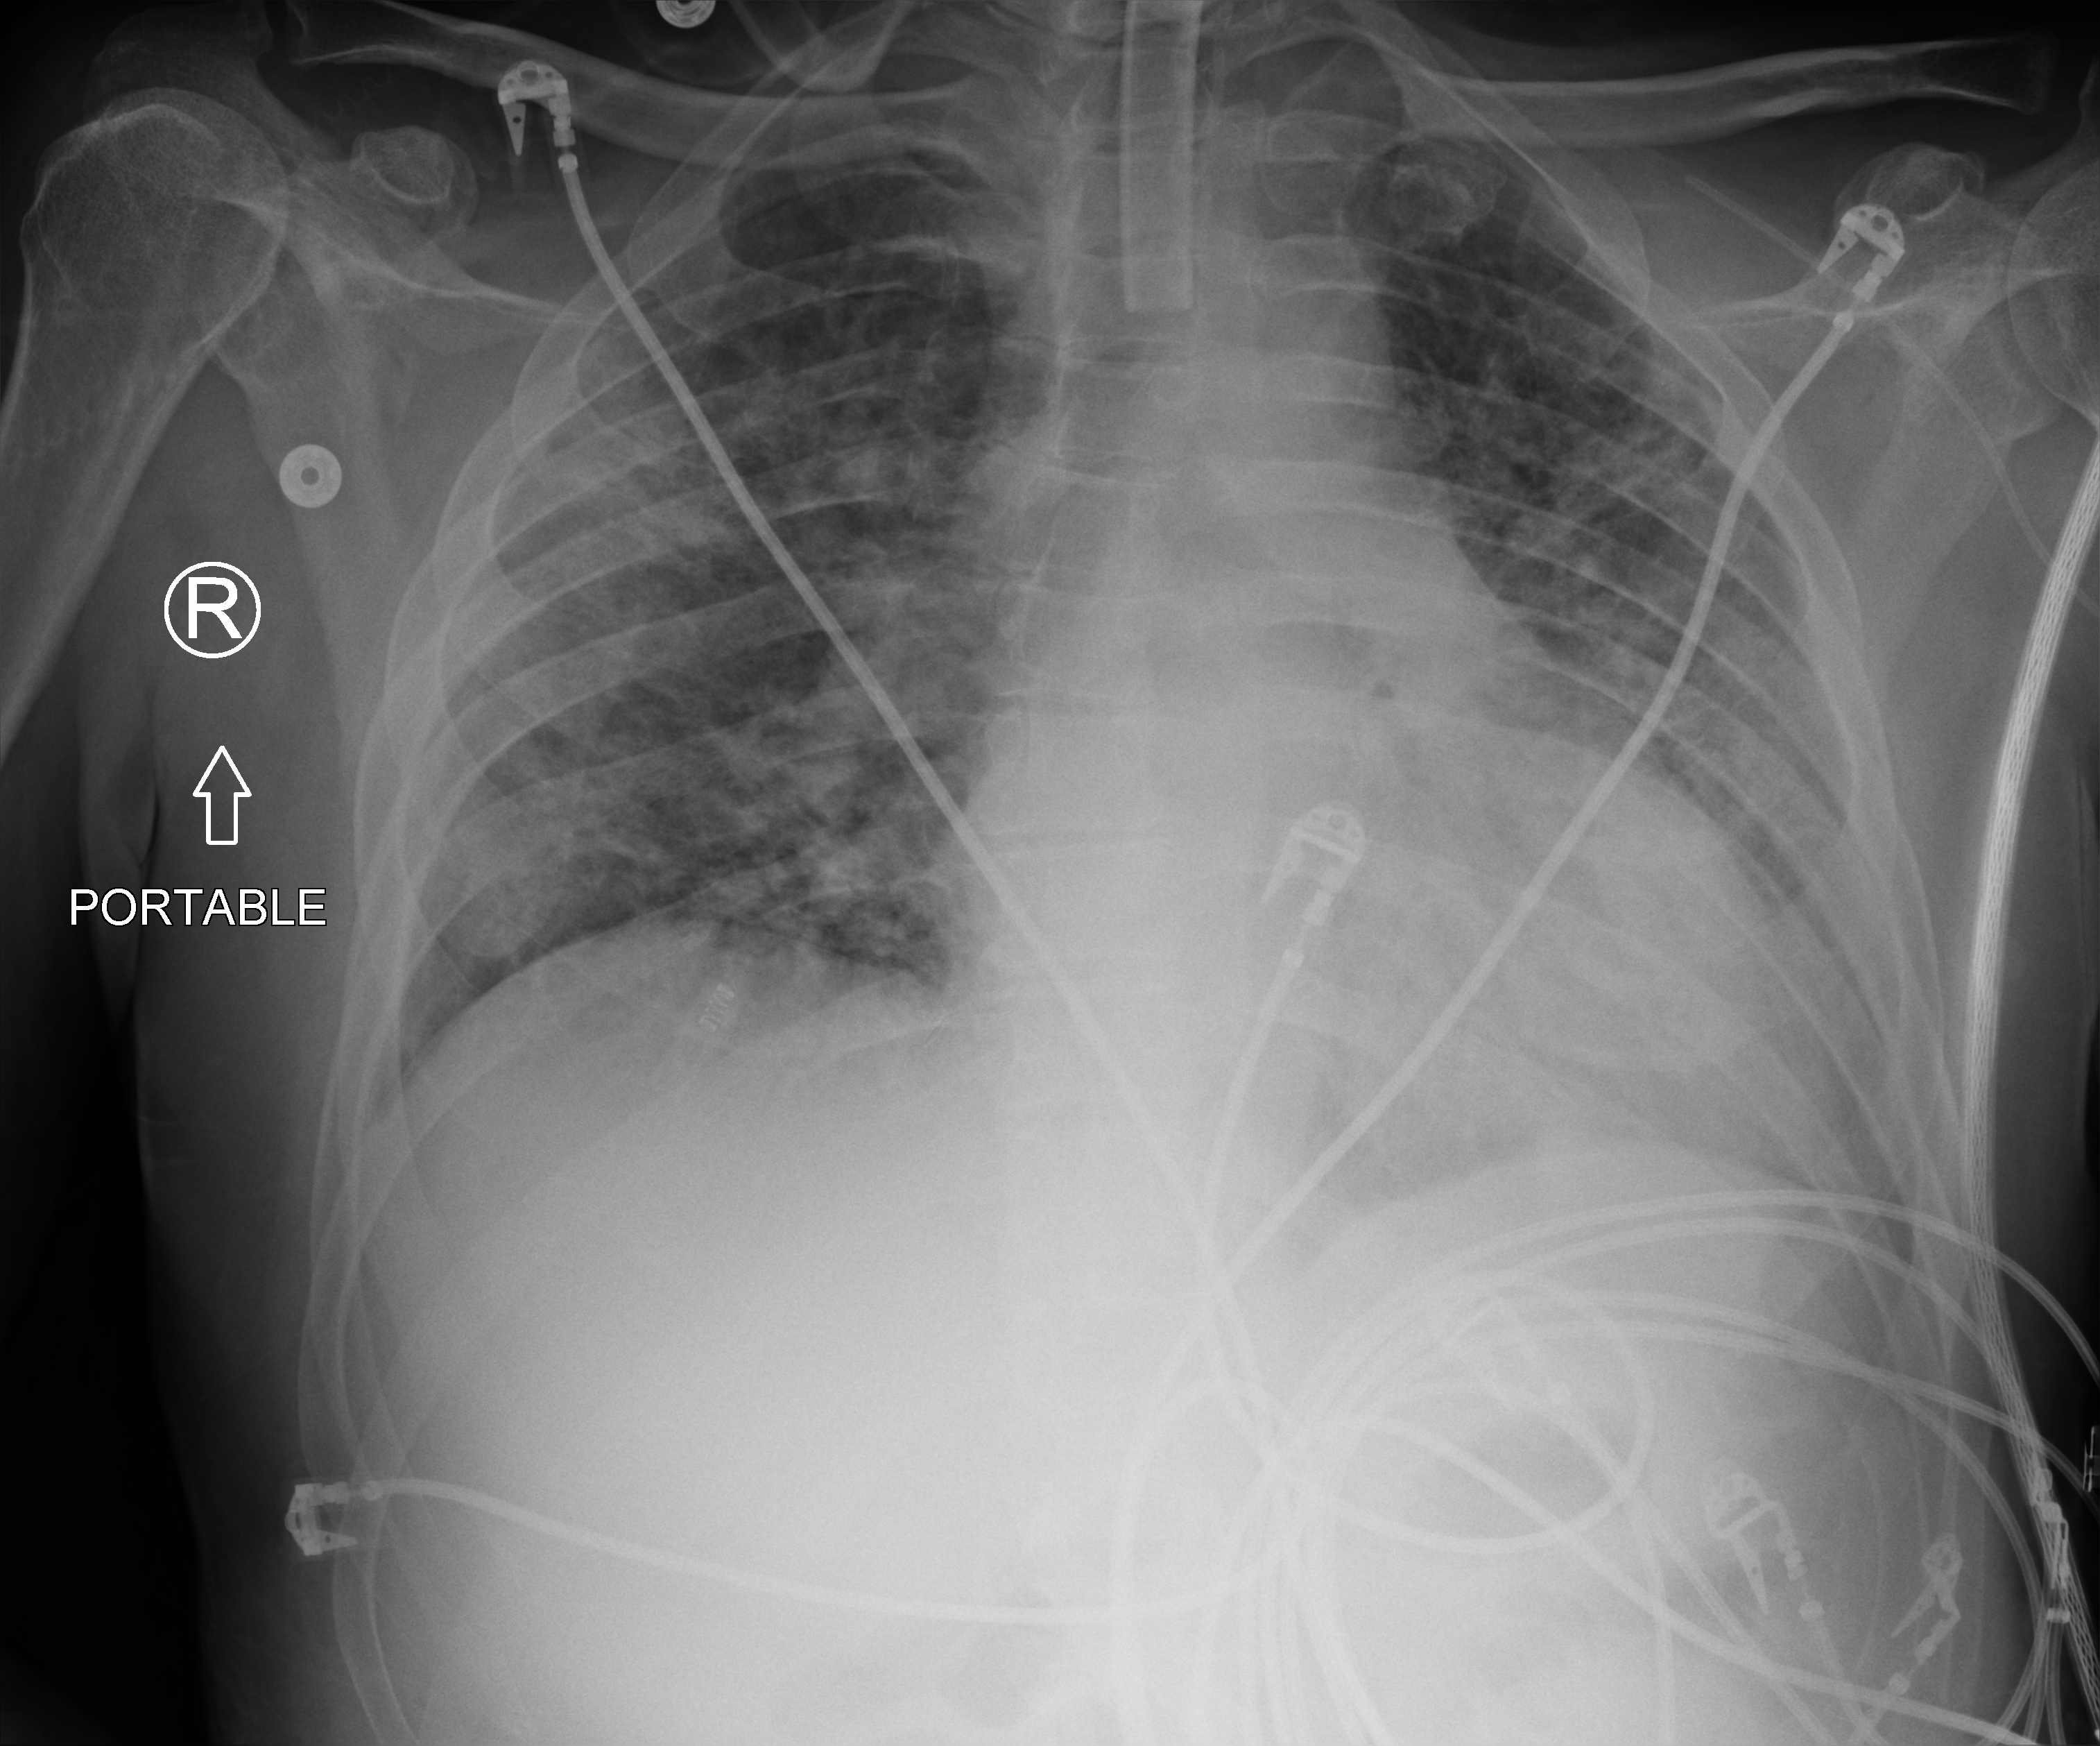
Portable chest radiograph, anteroposterior (AP) projection. Male patient hospitalised with COVID-19, age 18–59 years.
Hospital-stay facts (about this admission, not read from this image; timing relative to this image not recorded): mechanically ventilated during this hospital stay: yes; admitted to intensive care during this hospital stay: yes.